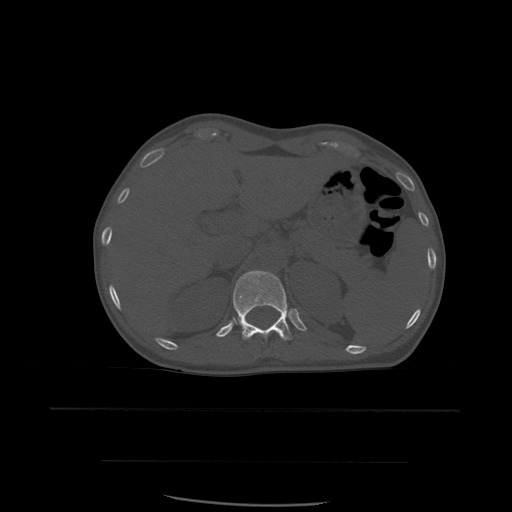
CT including the spine, one axial slice; position 274 of 574 along the scan axis; bone window (W 1800 / L 400 HU); 512 × 512 image matrix, field of view 392 × 392 mm. Patient age 48 years. Case-level facts recorded for this patient, not image findings: primary cancer: lung; vertebrae with lytic lesions (as recorded): T11.
Structures marked on this image (semi-automatically segmented with operator editing):
- T12 vertebra: bounding box <233,271,293,341> (left, top, right, bottom; pixels)